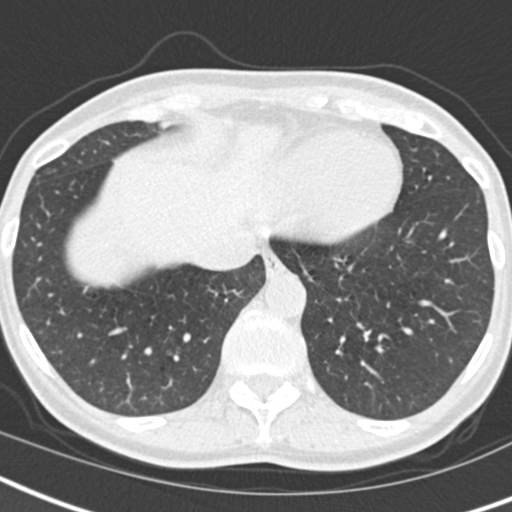
Low-dose screening chest CT, one axial slice. Position 50 of 173 along the scan axis. Reconstruction kernel B30f. 120 kVp. Lung window (W 1500 / L -600 HU). 2 mm slice thickness. 512 × 512 image matrix, field of view 293 × 293 mm.
Outlined on this slice (expert manual segmentation):
- lesion 1 (tumor, lower lobe of left lung): bounding box (x1, y1, x2, y2) in pixels: (364, 330, 372, 338)